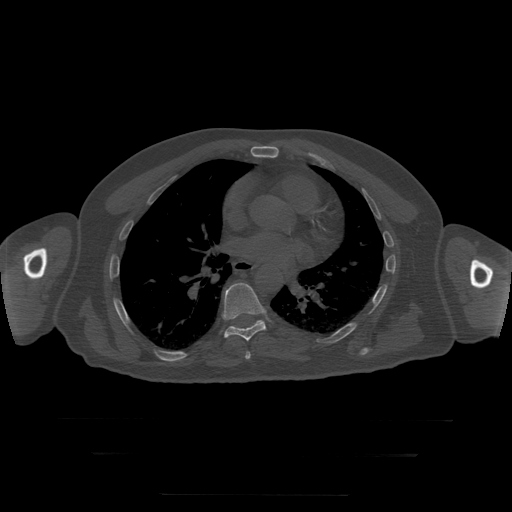
CT including the spine, one axial slice. Slice 165 of 397 in the series (ordered by position). Bone window (W 1800 / L 400 HU). 512 × 512 image matrix. Patient age 73 years. Case-level facts recorded for this patient, not image findings: primary cancer: prostate.
Outlined on this slice (semi-automatic segmentation, software-assisted and operator-edited):
- T7 vertebra: box from (x=245, y=352) to (x=251, y=360) px
- T8 vertebra: (x=222, y=283)–(x=266, y=341)
- T9 vertebra: (x=257, y=321)–(x=261, y=323)